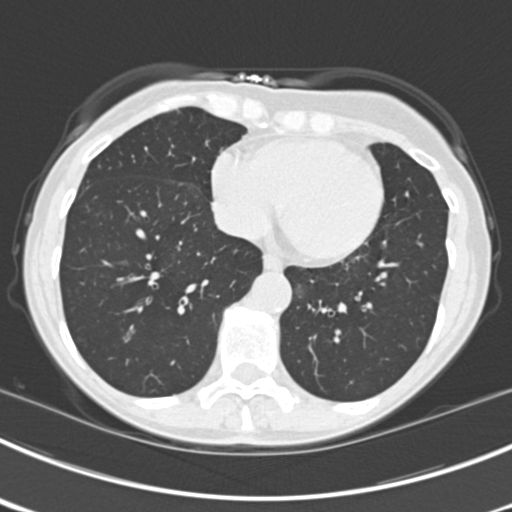
Low-dose screening chest CT, axial slice. Third annual screen. Lung window (W 1500 / L -600 HU). 512 × 512 image matrix, field of view 302 × 302 mm. Female, age 63 years at enrolment. Current smoker at enrolment.
Expert-annotated lung lesion, bounding box [x1, y1, x2, y2] px = [103, 312, 149, 360]. The screening reader recorded 9 non-calcified nodules or masses ≥4 mm on this exam; which of them this box marks is not recorded. Official screen result: positive, other. Lung cancer was diagnosed 15 days after this screen: bronchiolo-alveolar adenocarcinoma, NOS, right upper lobe, right middle lobe, right lower lobe, left upper lobe, left lower lobe, moderately differentiated (G2), stage IV (AJCC 6th edition).